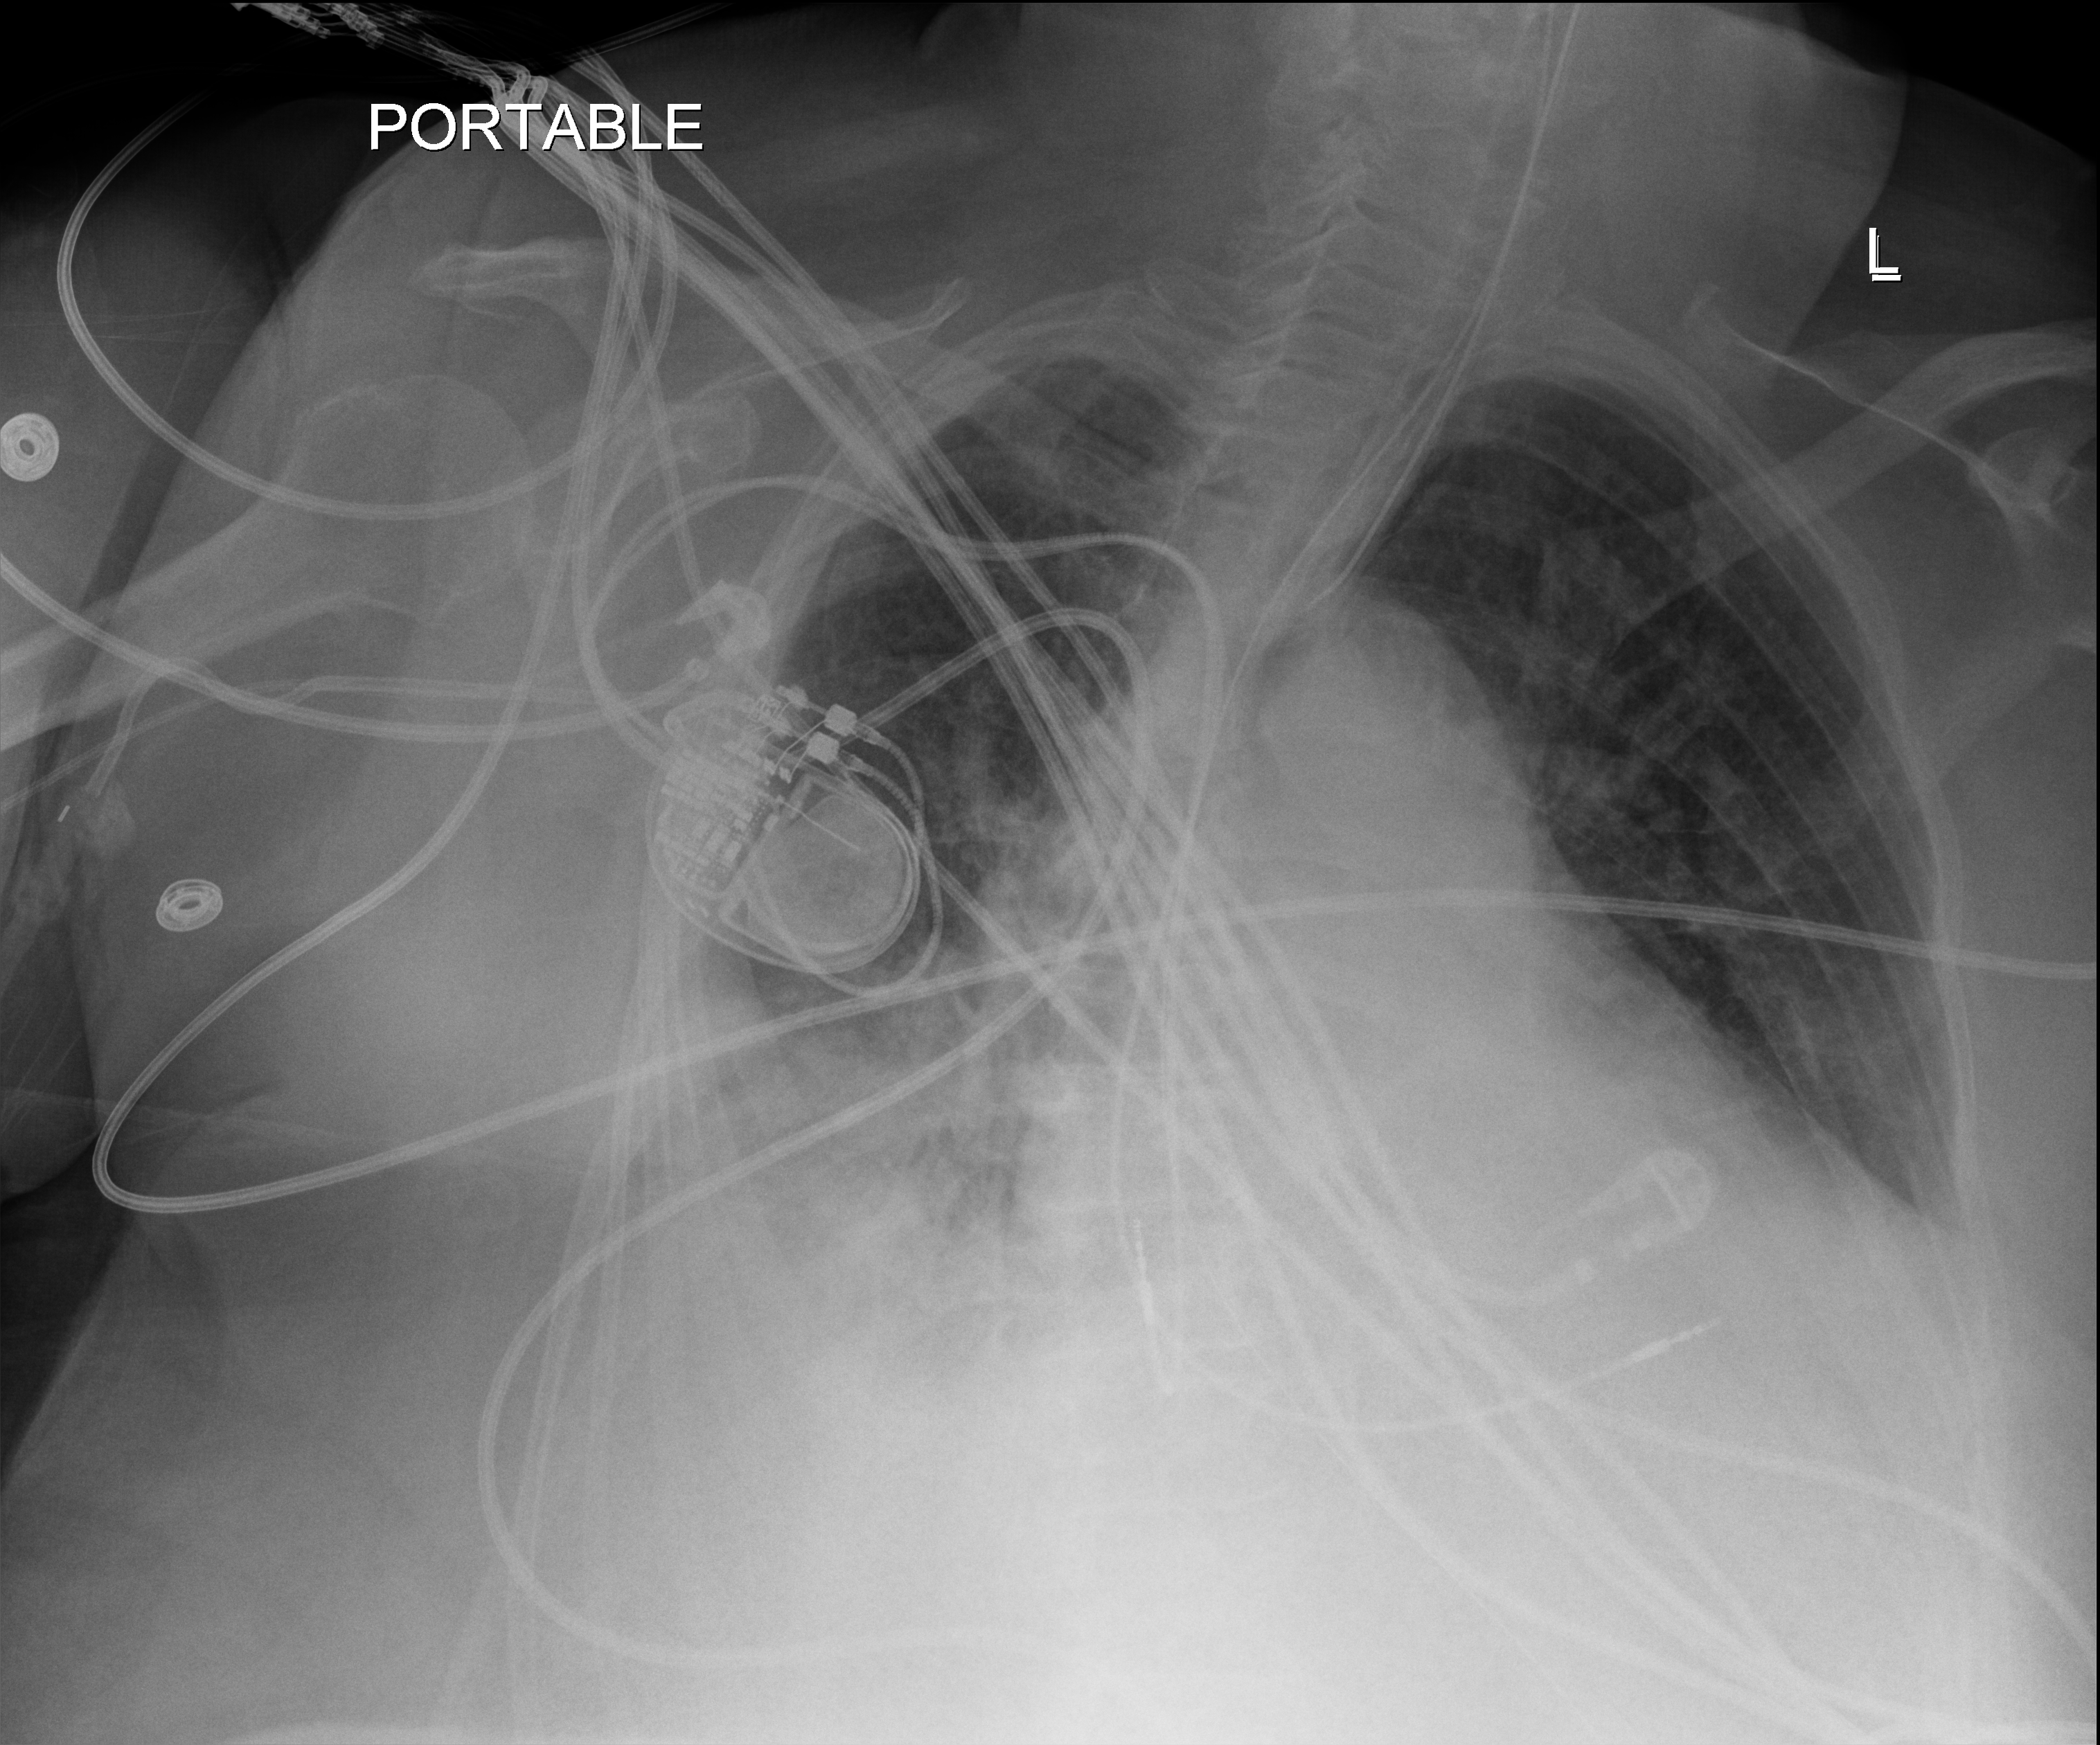
Portable chest radiograph, anteroposterior (AP) projection. Female patient hospitalised with COVID-19, age 75–90 years.
Admission-level facts for this patient (not findings on this image; timing relative to this image not recorded):
- length of hospital stay: 21 days
- mechanically ventilated during this hospital stay: yes